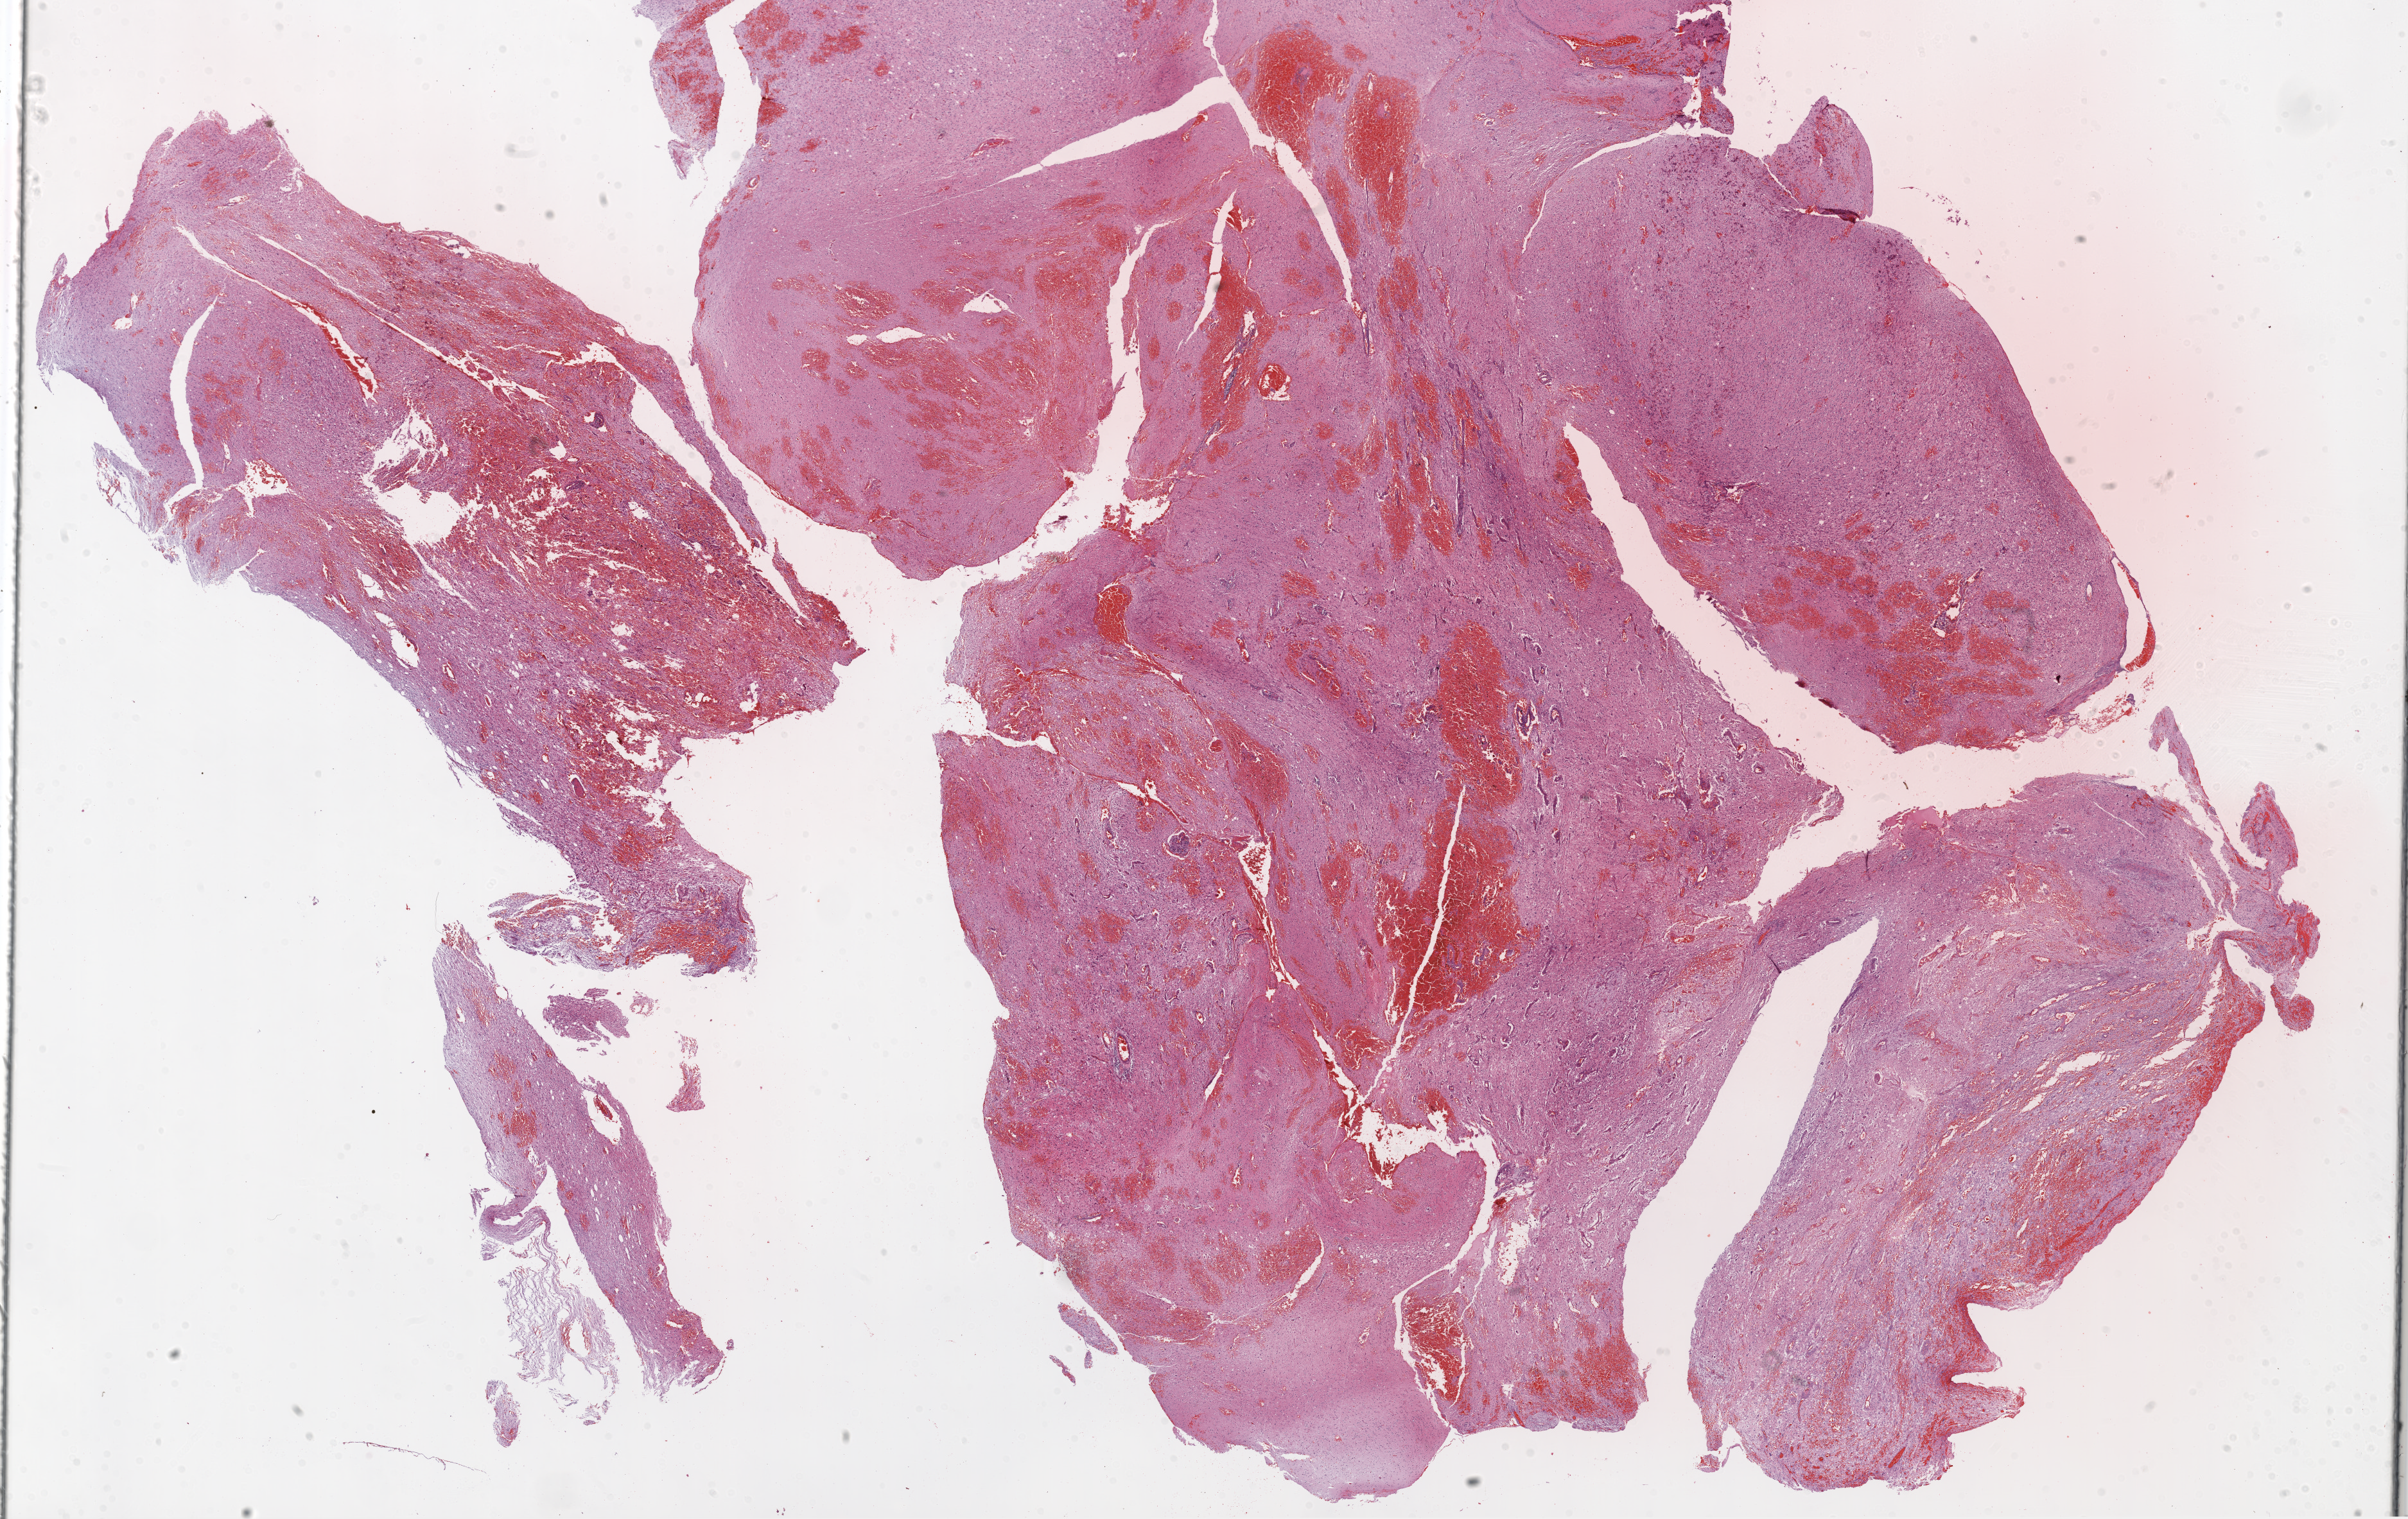
Whole-slide histology image, H&E, shown as a low-resolution overview of the whole scanned area (about 30.1 x 19.0 mm, slide scanned at 20x), FFPE section, primary tumour sample from the brain. Male patient; age at initial diagnosis 58 years.
- diagnosis: Glioblastoma